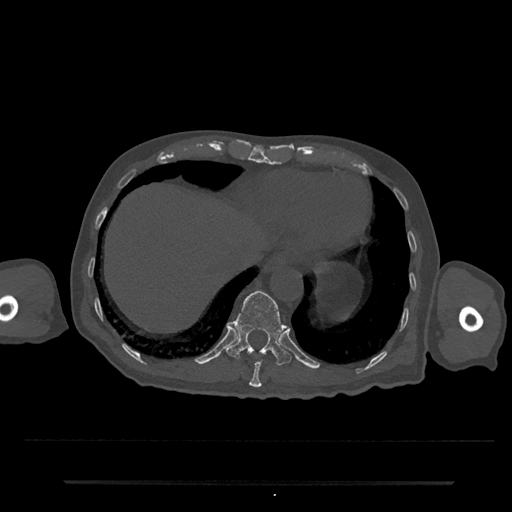
CT including the spine, one axial slice. Slice 271 of 797 in the series (ordered by position). Reconstruction kernel Br40s/3. Bone window (W 1800 / L 400 HU). 512 × 512 image matrix, field of view 427 × 427 mm. Patient: male, 74 years. From the clinical record (not read from this slice): primary cancer: prostate.
Structures marked on this image (semi-automatically segmented with operator editing):
- T10 vertebra: box from (x=249, y=358) to (x=262, y=388) px
- T11 vertebra: (x=226, y=290)–(x=292, y=366)